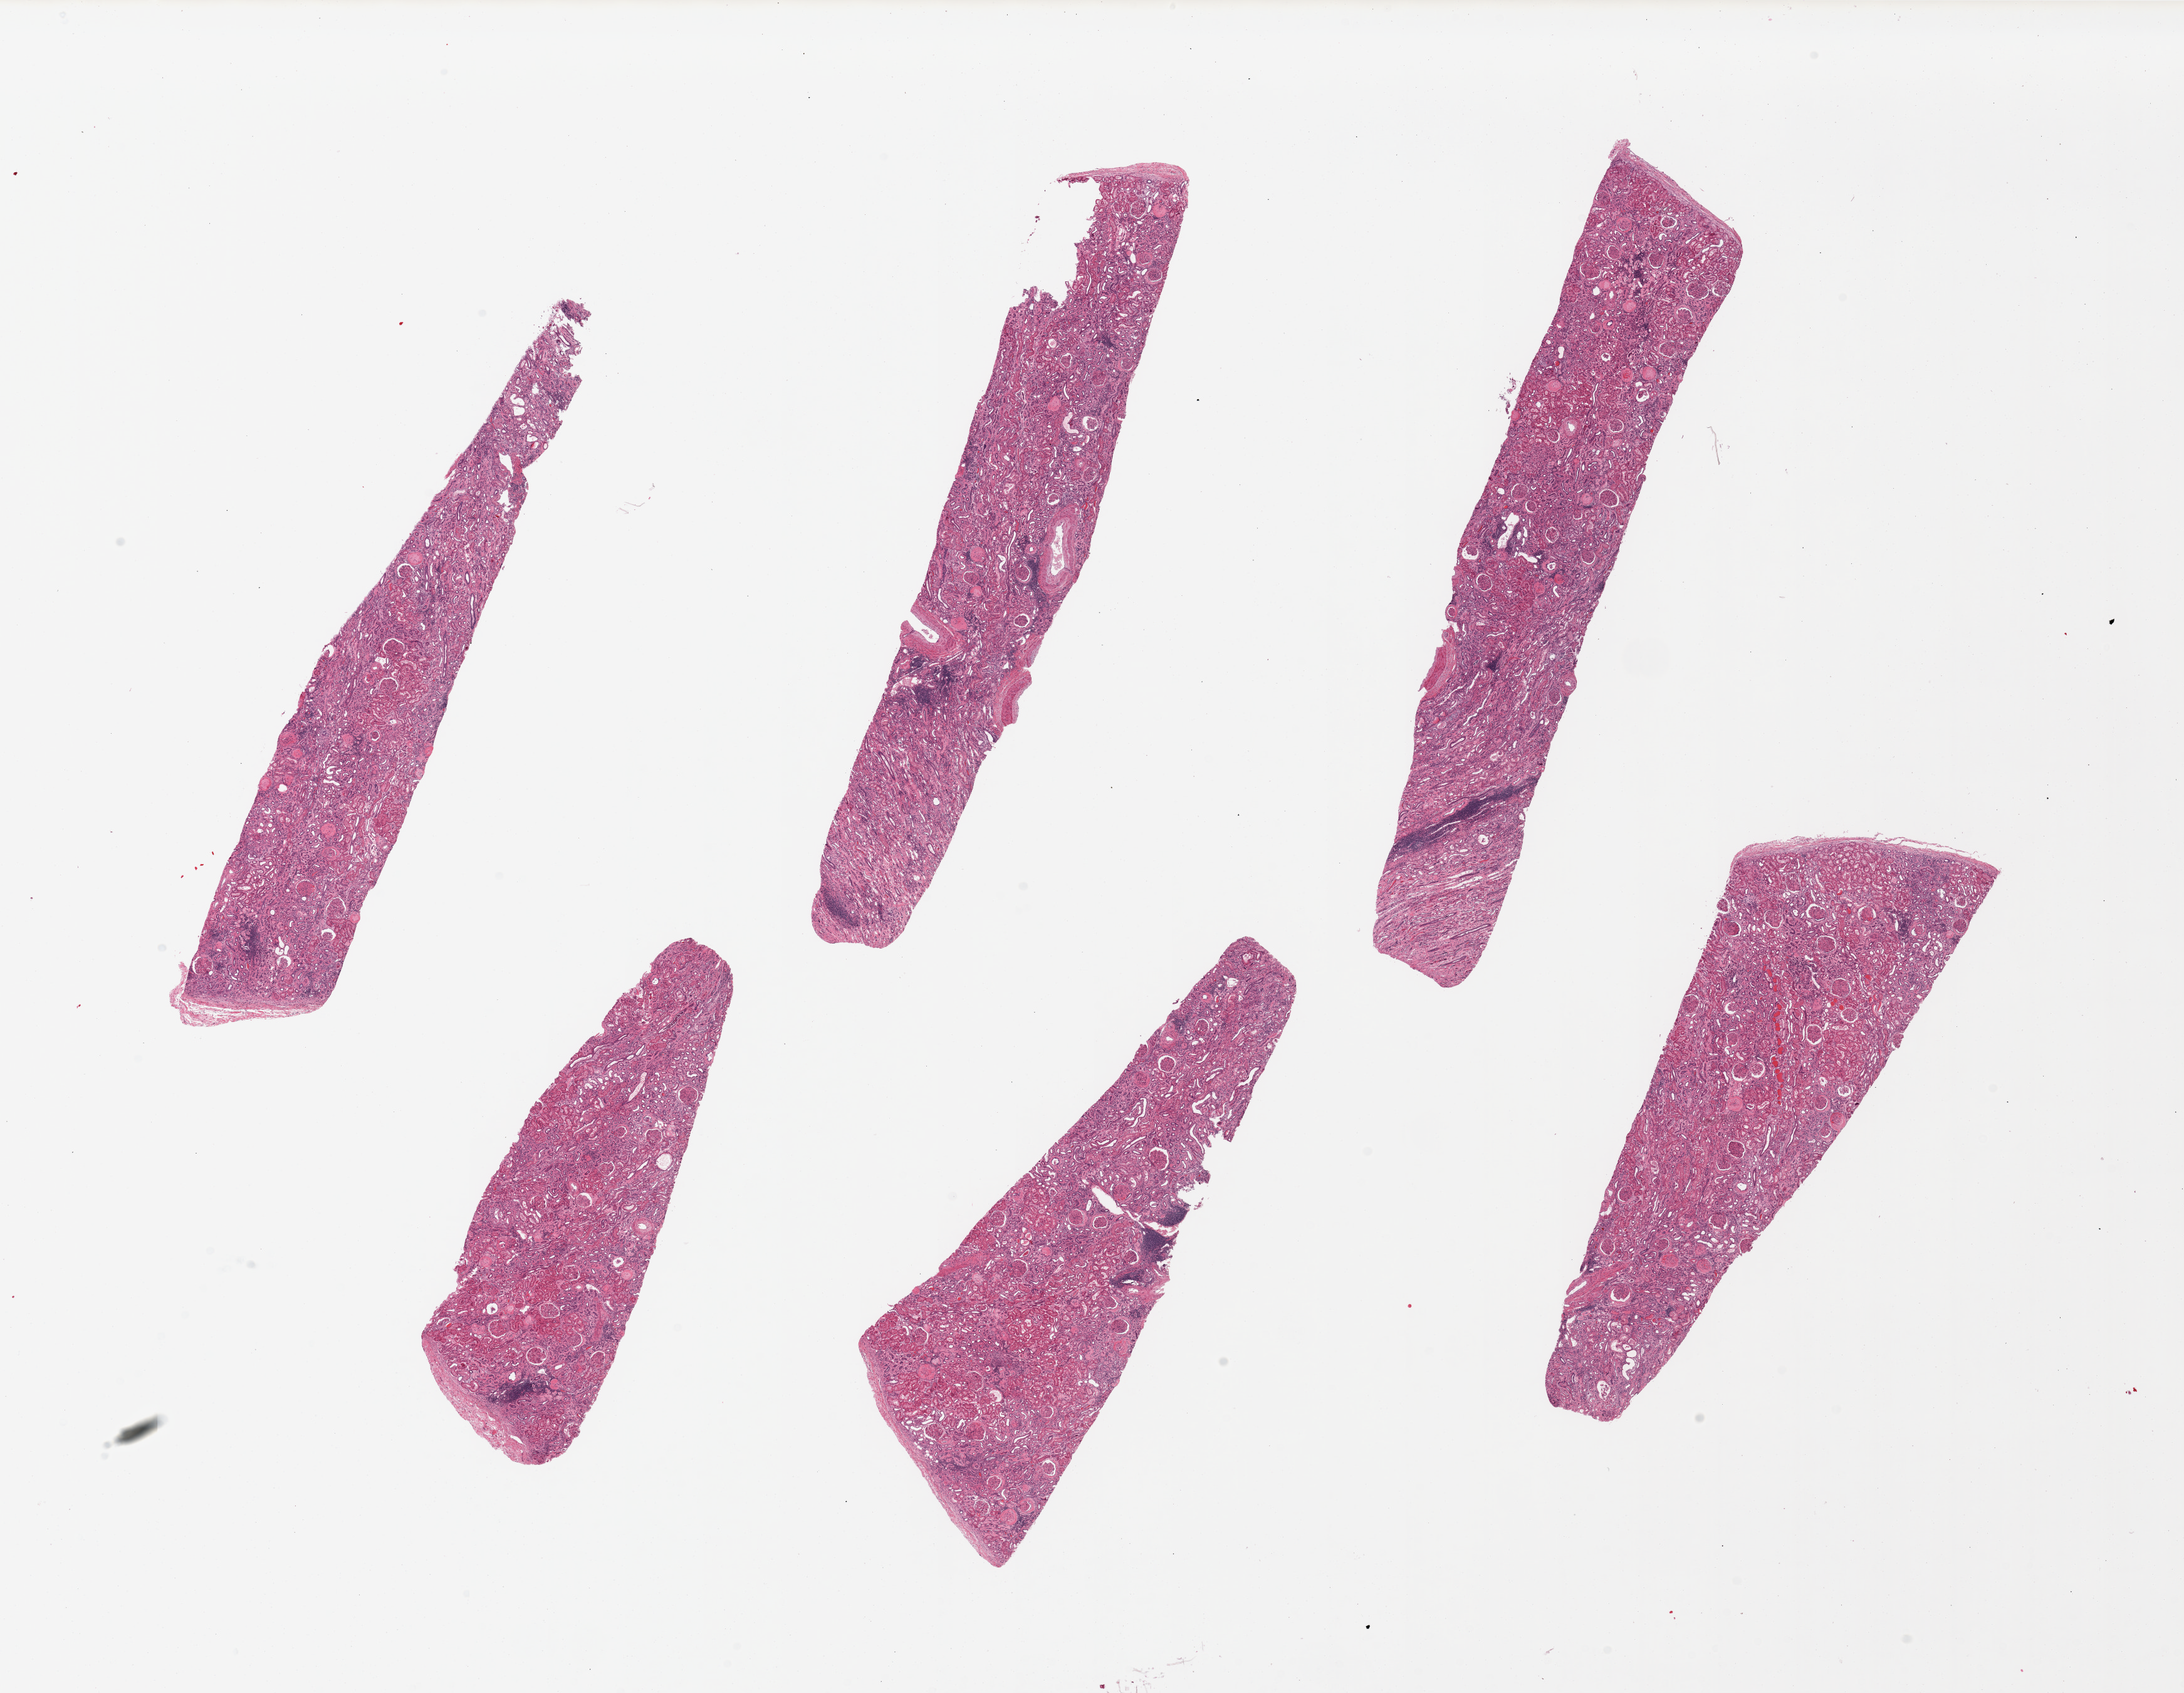
Digitized H&E-stained section, a low-resolution overview of the entire scanned area, about 27.6 x 21.4 mm; PAXgene-fixed, paraffin-embedded tissue; sampled site (target tissue): renal cortex; tissue donor sample. Male donor.
Review note (as recorded): 6 pieces. Characteristic lesions of diabetic glomerulosclerosis. Unusually well preserved tubules.